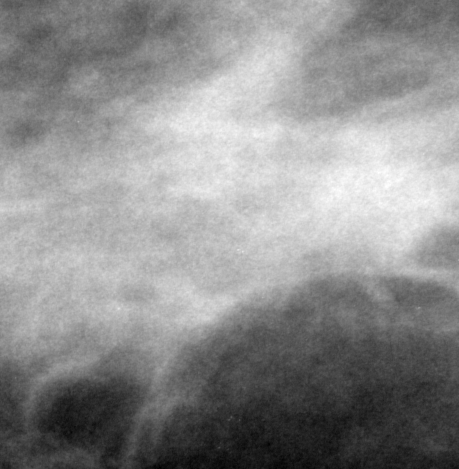
Region of interest cut from a scanned film mammogram (one marked finding); left breast; MLO view; BI-RADS breast density category 2 (scale 1–4).
Finding: mass, shape irregular, margins spiculated; BI-RADS assessment category 5; pathology result (as recorded, not read from the image): malignant.